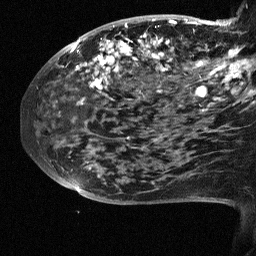
Breast MRI (dynamic contrast-enhanced), one sagittal slice; slice 22 of 64 in the series (ordered by position); dynamic contrast-enhanced study with each time point stored as its own series, time point 2 of 3 at this slice position (early post-contrast, ordered by acquisition time); 1.5 T; TE 4.5 ms, TR 11 ms; 2.5 mm slice thickness; 256 × 256 image matrix, field of view 200 × 200 mm. Female patient, age 38 years. Case-level facts recorded for this patient, not image findings: setting: breast cancer imaged before/during neoadjuvant chemotherapy; receptor status: HR-positive, HER2-negative.
Structures marked on this image (semi-automatically segmented with operator editing):
- analysis volume of interest (the breast-tissue region the enhancement analysis was run in; not a lesion): box from (x=88, y=18) to (x=252, y=126) px
- tumour enhancement mask (voxels above the 90 % enhancement threshold inside the analysis volume of interest): (x=91, y=19)–(x=252, y=100)